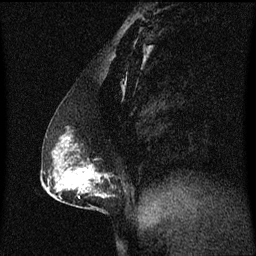
Breast MRI (dynamic contrast-enhanced), one sagittal slice. Slice 32 of 60 in the series (ordered by position). Dynamic contrast-enhanced series, image 2 of 3 at this slice position (ordered by acquisition). 1.5 T. TE 4.2 ms, TR 8.4 ms. 2 mm slice thickness. 256 × 256 image matrix, field of view 200 × 200 mm. Patient: female, 40 years. Case-level facts recorded for this patient, not image findings: setting: breast cancer imaged before/during neoadjuvant chemotherapy; receptor status: triple-negative.
Annotated regions visible in this slice (semi-automatic segmentation, software-assisted and operator-edited):
- analysis volume of interest (the breast-tissue region the enhancement analysis was run in; not a lesion): bounding box [x1, y1, x2, y2] px = [58, 126, 115, 211]
- tumour enhancement mask (voxels above the 70 % enhancement threshold inside the analysis volume of interest): [66, 138, 107, 197]